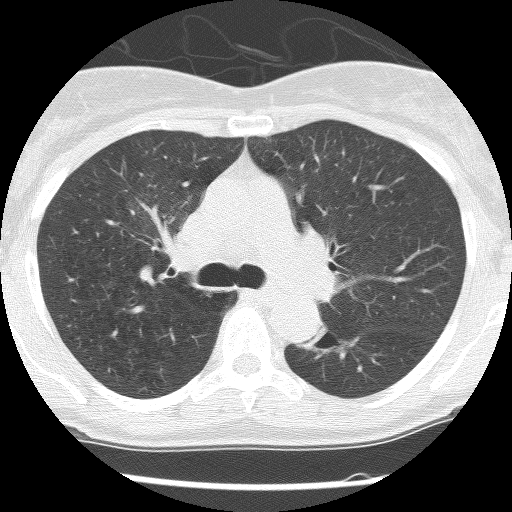
Axial slice from a low-dose chest CT screening exam, second screening round (one year after baseline), lung window (W 1500 / L -600 HU), 2.5 mm slice thickness, 512 × 512 image matrix, field of view 290 × 290 mm. Female participant, aged 62 years at enrolment.
• Expert reader's lesion annotation, bounding box [x1, y1, x2, y2] px = [295, 318, 350, 362].
• The exam's reader record, not a measurement of the box and not confirmed to be the same lesion: non-calcified nodule or mass ≥4 mm, right upper lobe, 30 × 30 mm, poorly defined margins, ground glass attenuation, pre-existing on the prior screen: yes; interval growth: no.
• Note: the box lies in the patient's left hemithorax on this image, whereas the reader's record names the right lung; they may be different findings.
• Participant outcome: lung cancer diagnosed 584 days after this screen (after the third annual screen) — squamous cell carcinoma, NOS, left lower lobe, stage IIIB (AJCC 6th edition), 31 mm at pathology.